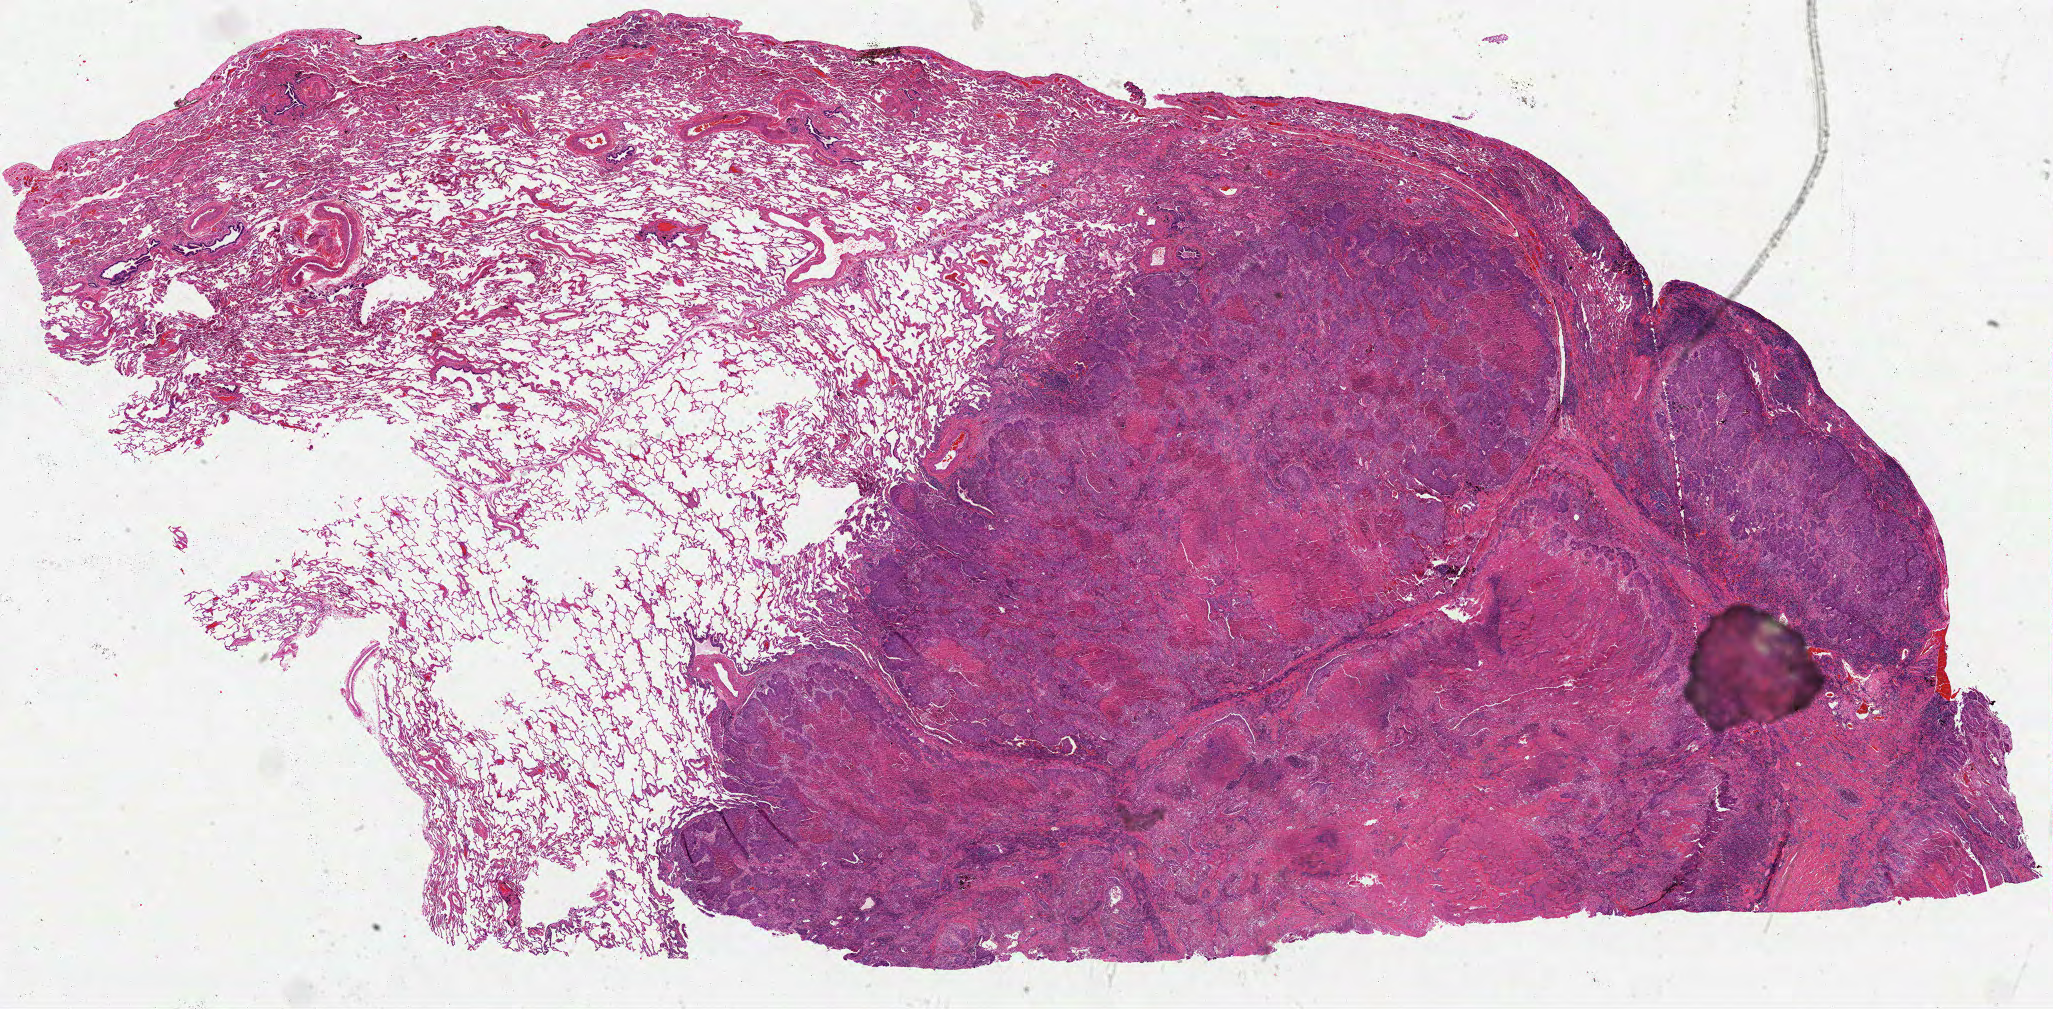
Digitized H&E tissue section (whole slide) — low-resolution overview of the scanned area, about 33.1 x 16.3 mm (from a 40x scan). Formalin-fixed paraffin-embedded (FFPE) diagnostic section. Lung, primary tumour sample. Male, age 68 years at initial diagnosis.
AJCC pathologic stage: IB (6th edition). Laterality: right. Pathologic diagnosis: Squamous cell carcinoma, NOS. TNM: T2 N0 M0.